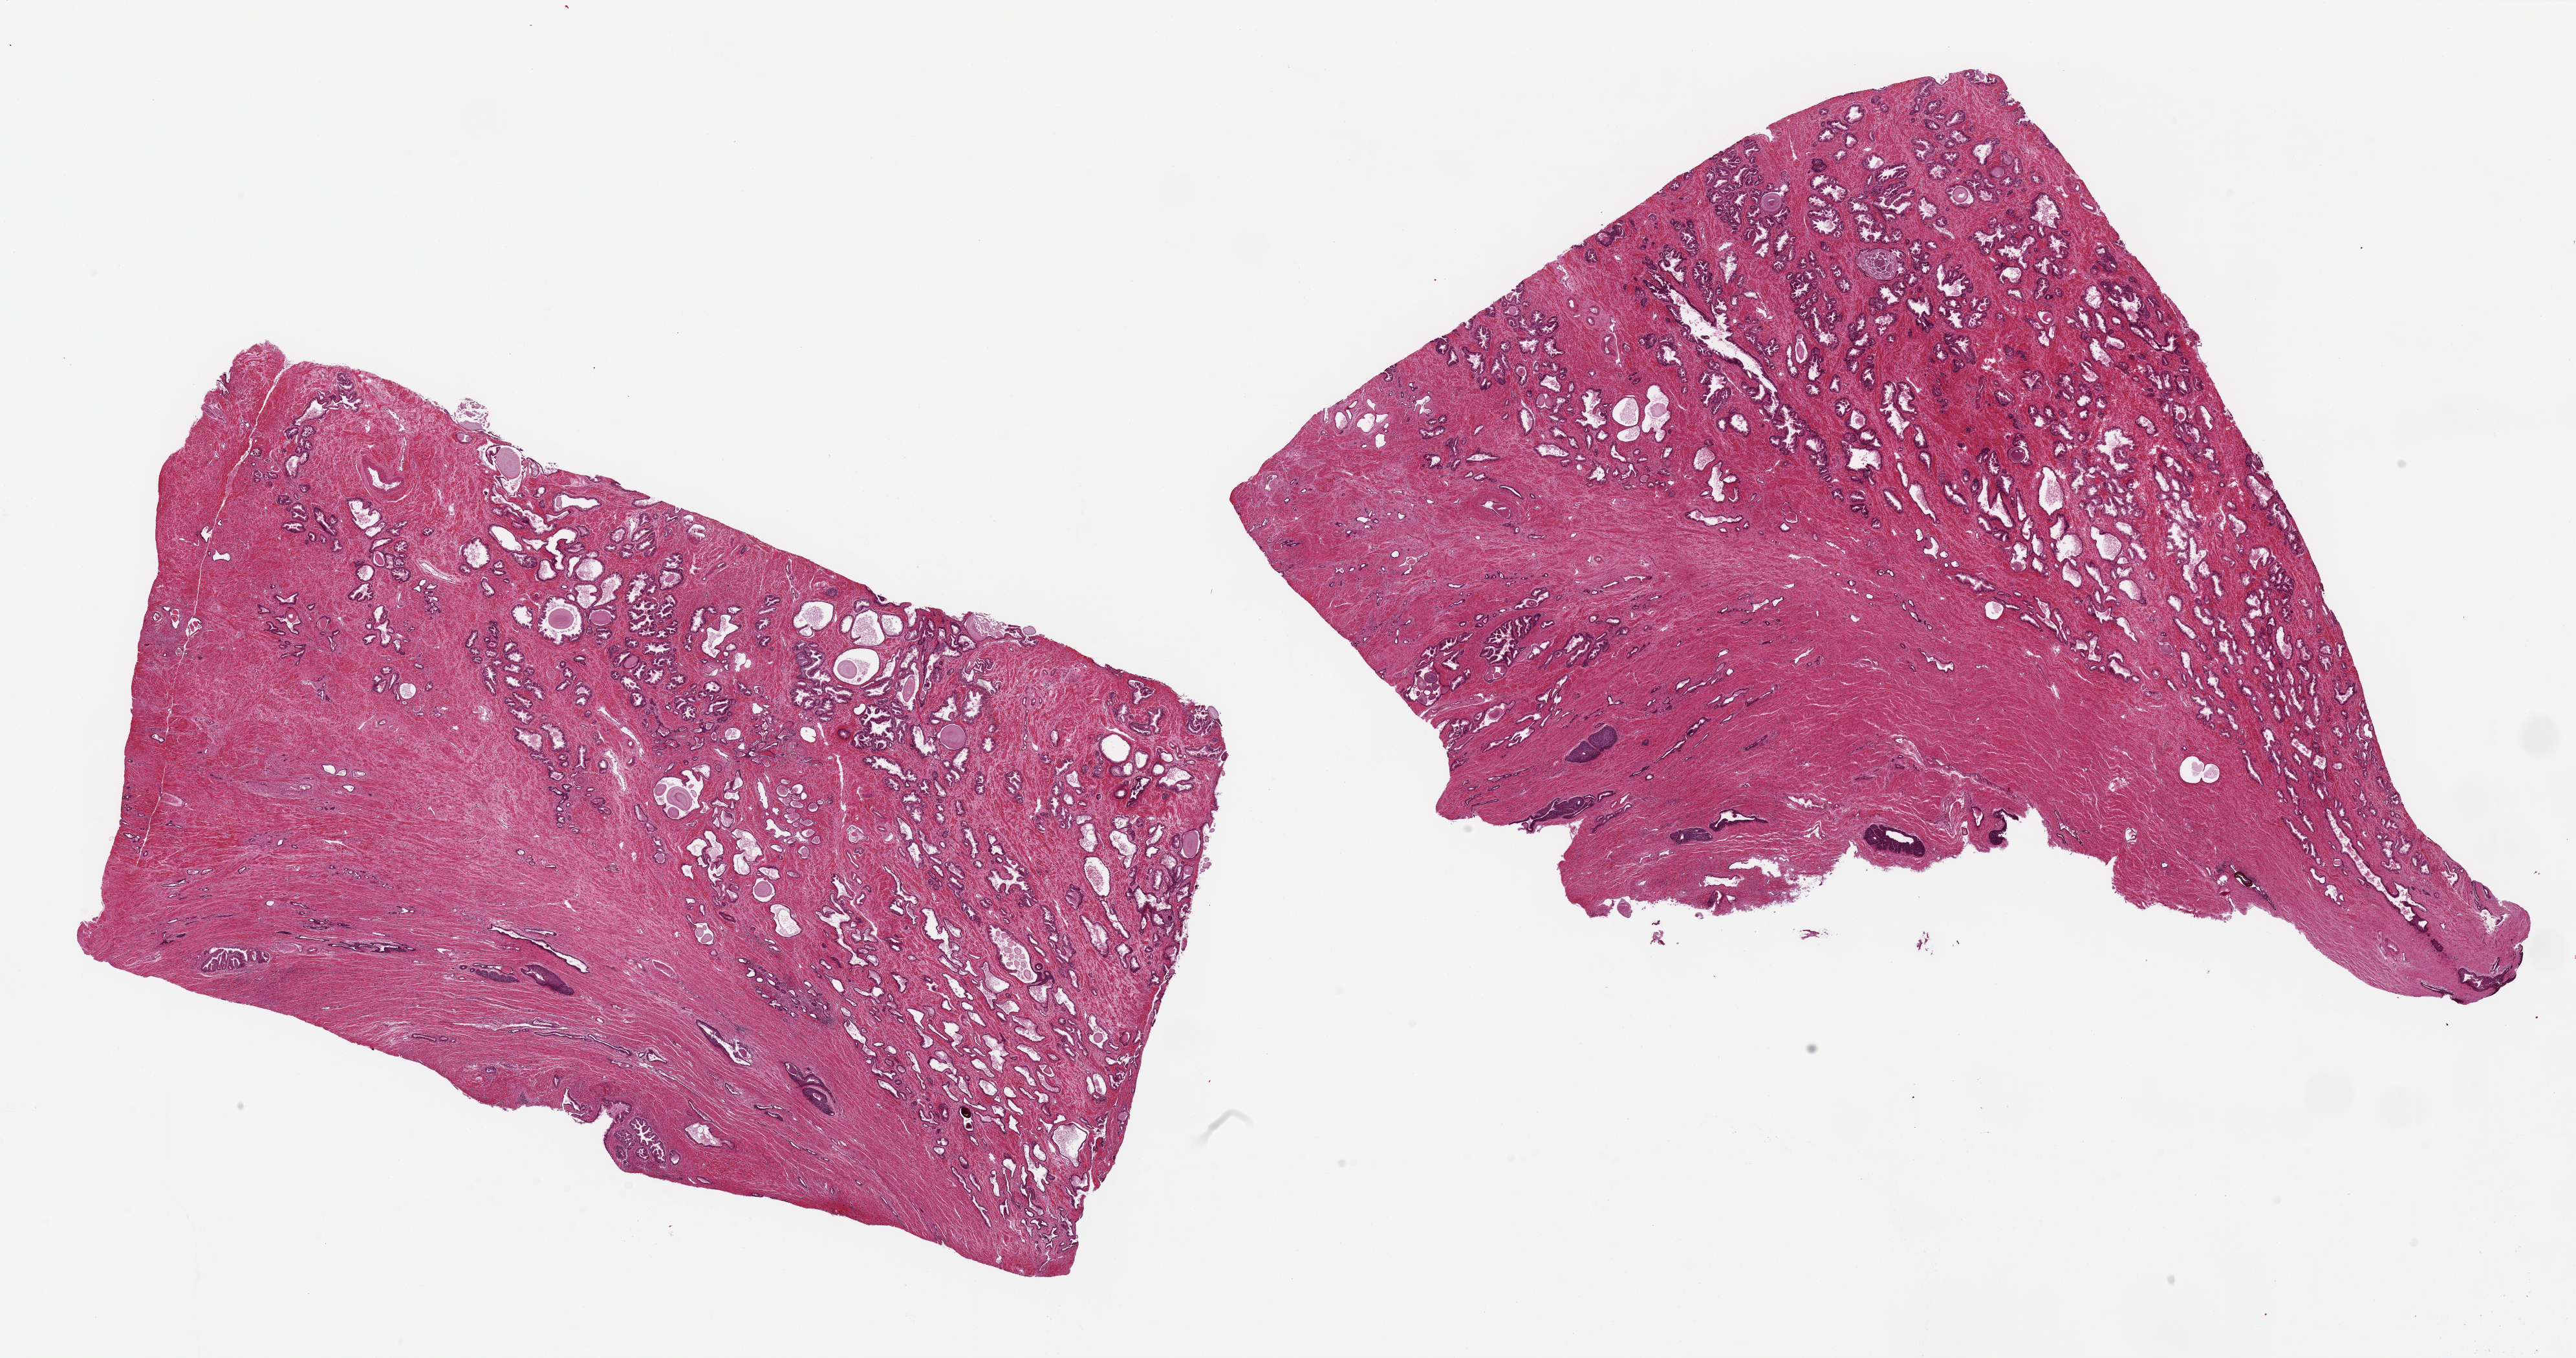
Whole-slide image, H&E stain, brightfield, a low-resolution overview of the entire scanned area, about 31.5 x 16.6 mm (from a 20x scan); PAXgene-fixed, paraffin-embedded tissue; target tissue: prostate; tissue donor sample. Donor: male.
Reviewer comment on this tissue sample: 2 pieces 13x10 & 13x7 mm; glandular and stromal hyperplasia; a few urethral structures along one side of each piece.